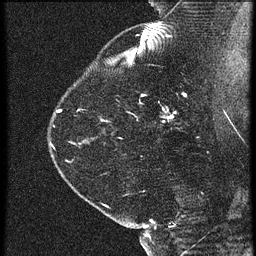
Breast MRI (dynamic contrast-enhanced), one sagittal slice; position 46 of 60 along the scan axis; 3 images stored at this slice position (order not interpretable as contrast timing); 1.5 T; TE 4.2 ms, TR 21.3 ms; 256 × 256 image matrix, field of view 180 × 180 mm. Patient: female, 42 years. From the clinical record (not read from this slice): setting: breast cancer imaged before/during neoadjuvant chemotherapy; receptor status: HER2-positive.
Outlined on this slice (semi-automatically segmented with operator editing):
- analysis volume of interest (the breast-tissue region the enhancement analysis was run in; not a lesion): bounding box [x1, y1, x2, y2] px = [122, 82, 195, 147]
- tumour enhancement mask (voxels above the 90 % enhancement threshold inside the analysis volume of interest): [162, 94, 184, 117]